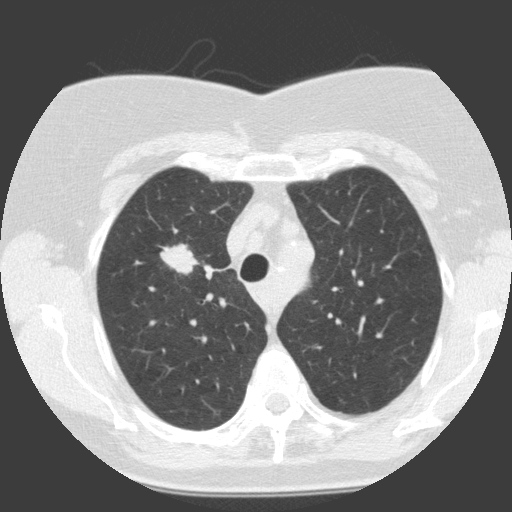
Chest CT (low-dose screening protocol), one axial image; baseline screening round; lung window (W 1500 / L -600 HU); 2 mm slice thickness. Female, age 68 years at enrolment. Current smoker at enrolment.
Expert reader's lesion annotation, bounding box (x1, y1, x2, y2) in pixels: (156, 236, 207, 283). The exam's reader record, not a measurement of the box and not confirmed to be the same lesion: non-calcified nodule or mass ≥4 mm, right upper lobe, 19 × 12 mm, smooth margins, soft tissue attenuation. Later outcome: lung cancer diagnosed 30 days after this screen — squamous cell carcinoma, NOS, right upper lobe, moderately differentiated (G2), stage IA (AJCC 6th edition), 28 mm at pathology.